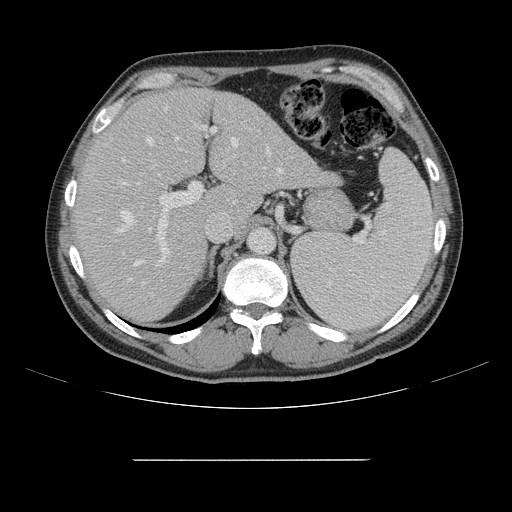
Contrast-enhanced abdominal CT, one axial slice; slice 104 of 164 in the series (ordered by position); intravenous contrast given; soft-tissue window (W 400 / L 40 HU); 2.5 mm slice thickness; 512 × 512 image matrix, field of view 404 × 404 mm. Male patient, age 54 years. Case-level facts recorded for this patient, not image findings: diagnosis: colorectal cancer liver metastases, imaged before liver resection; multiple liver metastases: yes.
Outlined on this slice (manually delineated by an expert):
- hepatic veins: box from (x=117, y=138) to (x=283, y=267) px
- liver: (x=75, y=88)–(x=334, y=324)
- planned liver remnant (the part of the liver to remain after resection): (x=75, y=88)–(x=239, y=323)
- portal vein (with intrahepatic branches): (x=119, y=105)–(x=218, y=298)